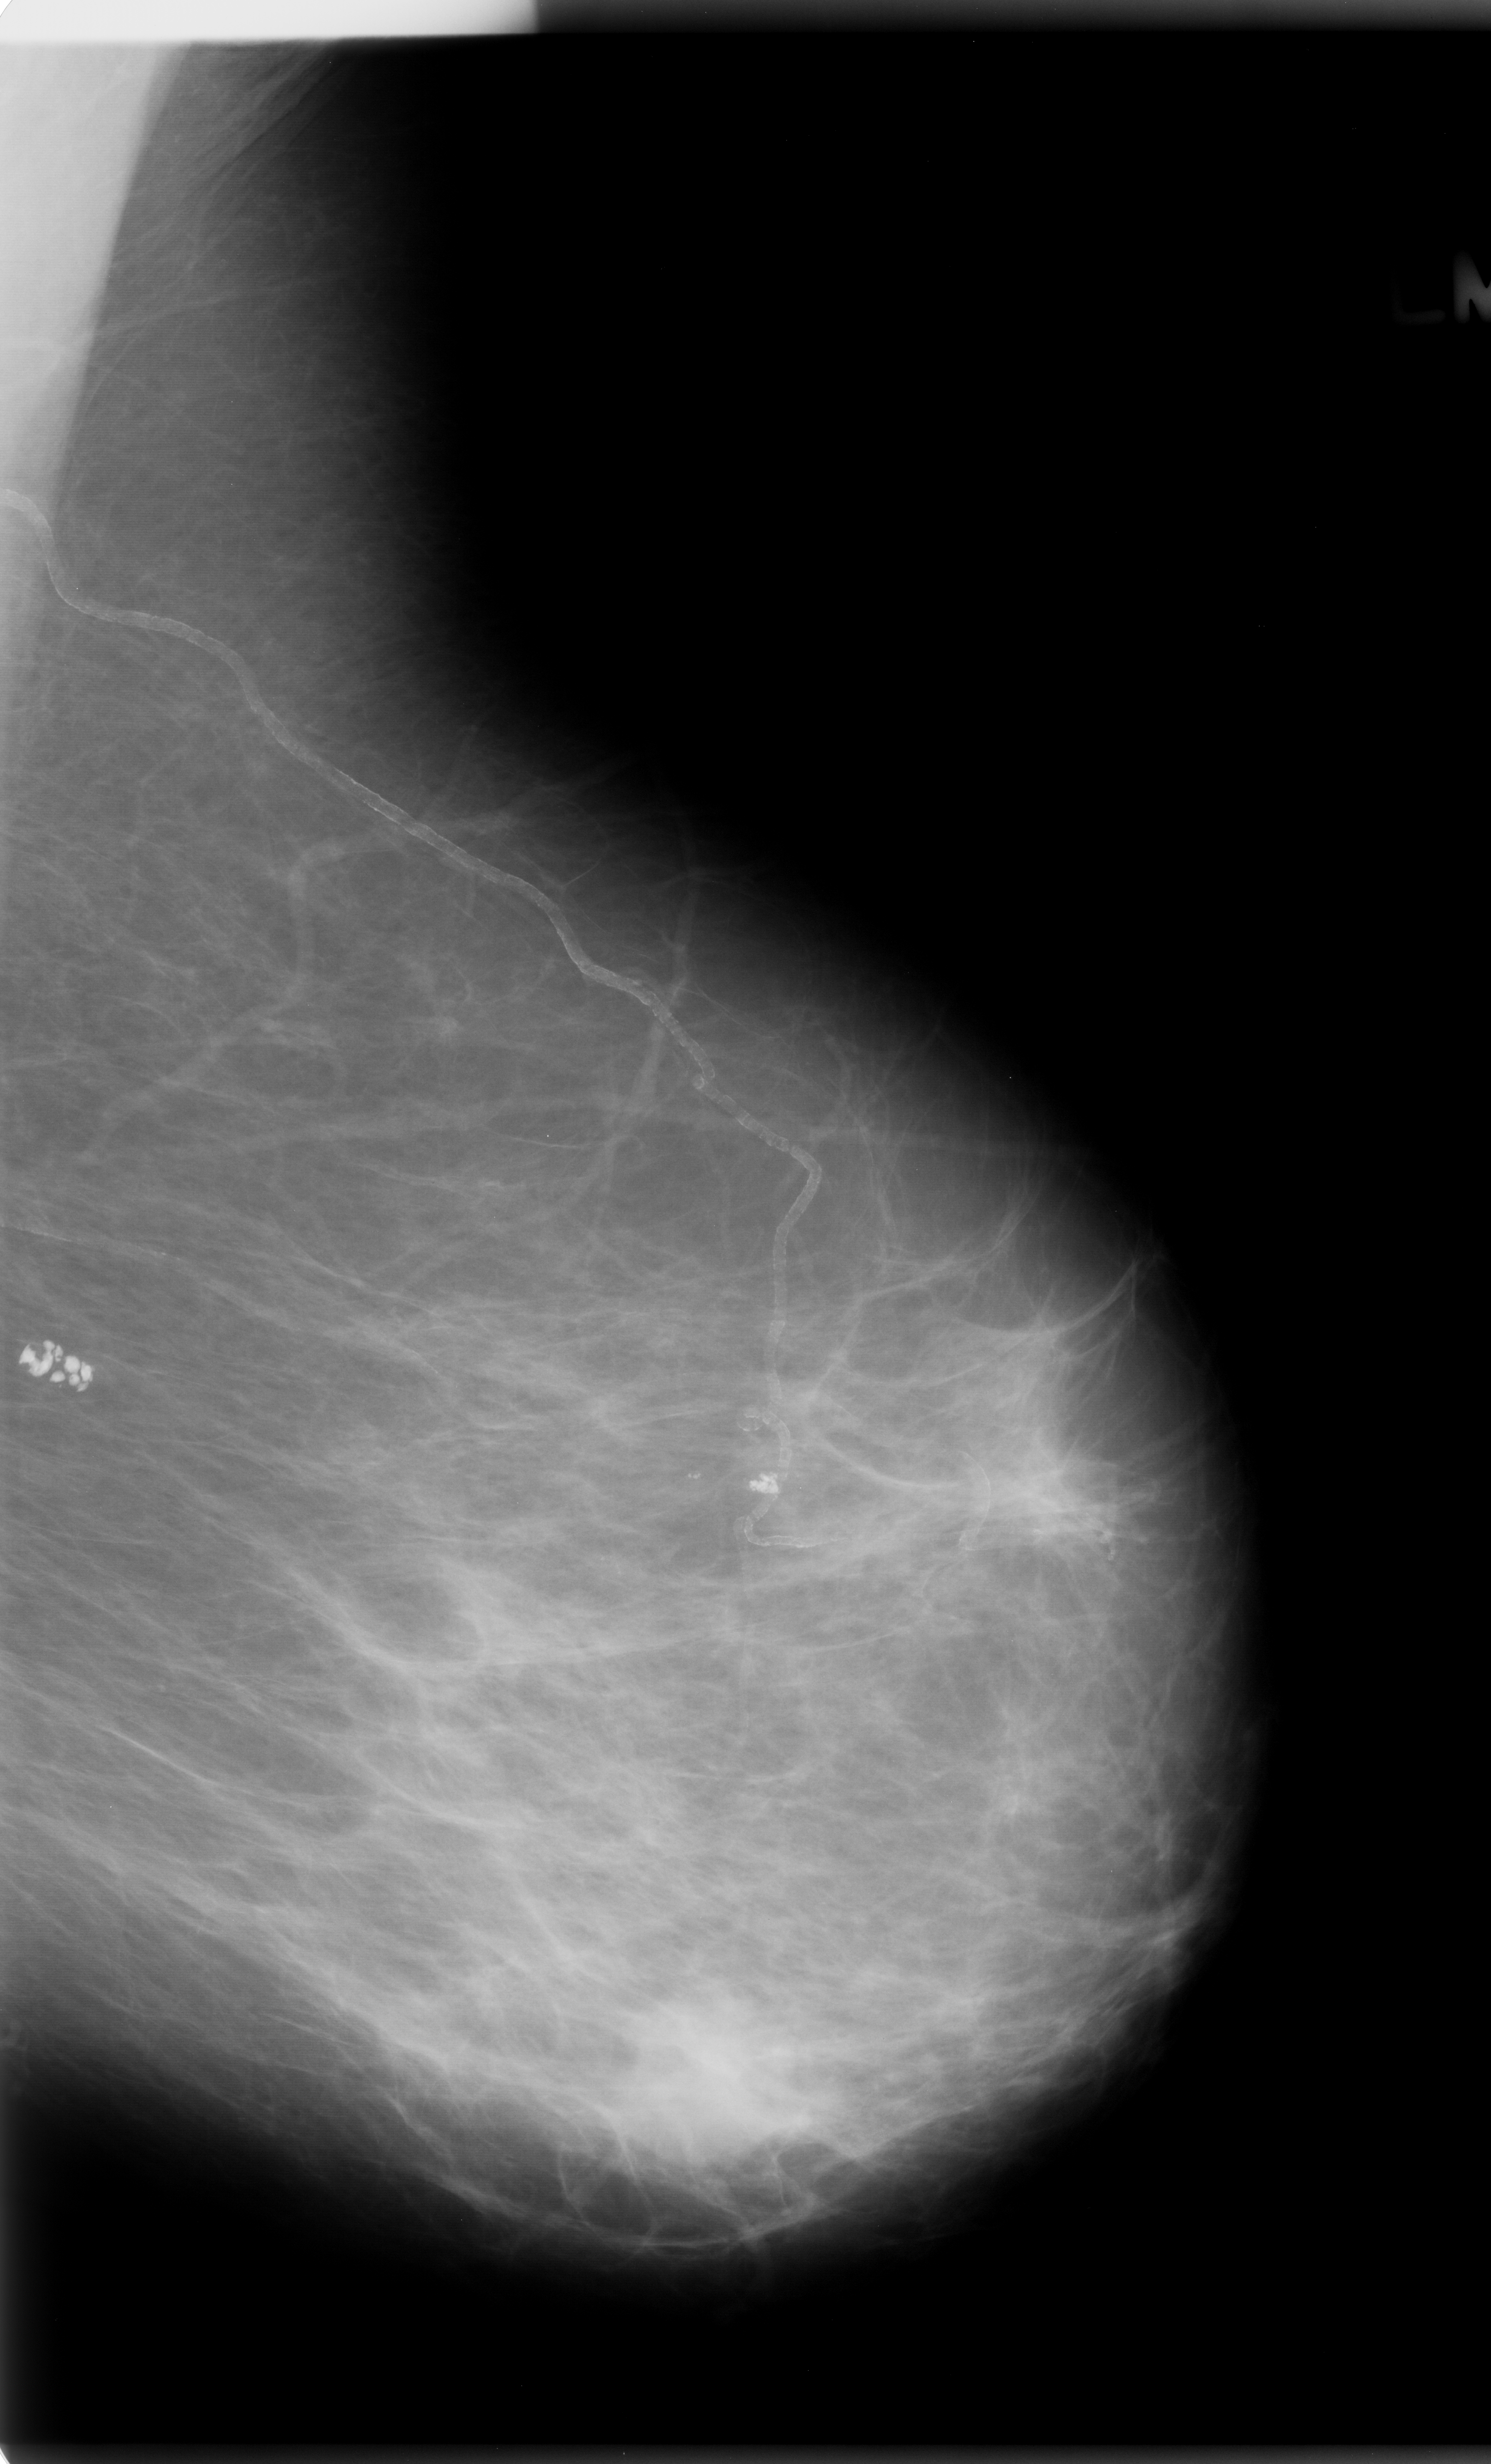
Digitized screen-film mammogram; left breast; mediolateral oblique (MLO) view; breast composition: almost entirely fatty (BI-RADS density category 1 of 4); 1491 × 2464 image matrix.
Marked abnormalities (boxes around the expert regions of interest):
- mass, shape lobulated, margins microlobulated; BI-RADS assessment category 5; pathology (as recorded): malignant: bounding box (x1, y1, x2, y2) in pixels: (618, 2008, 799, 2184)